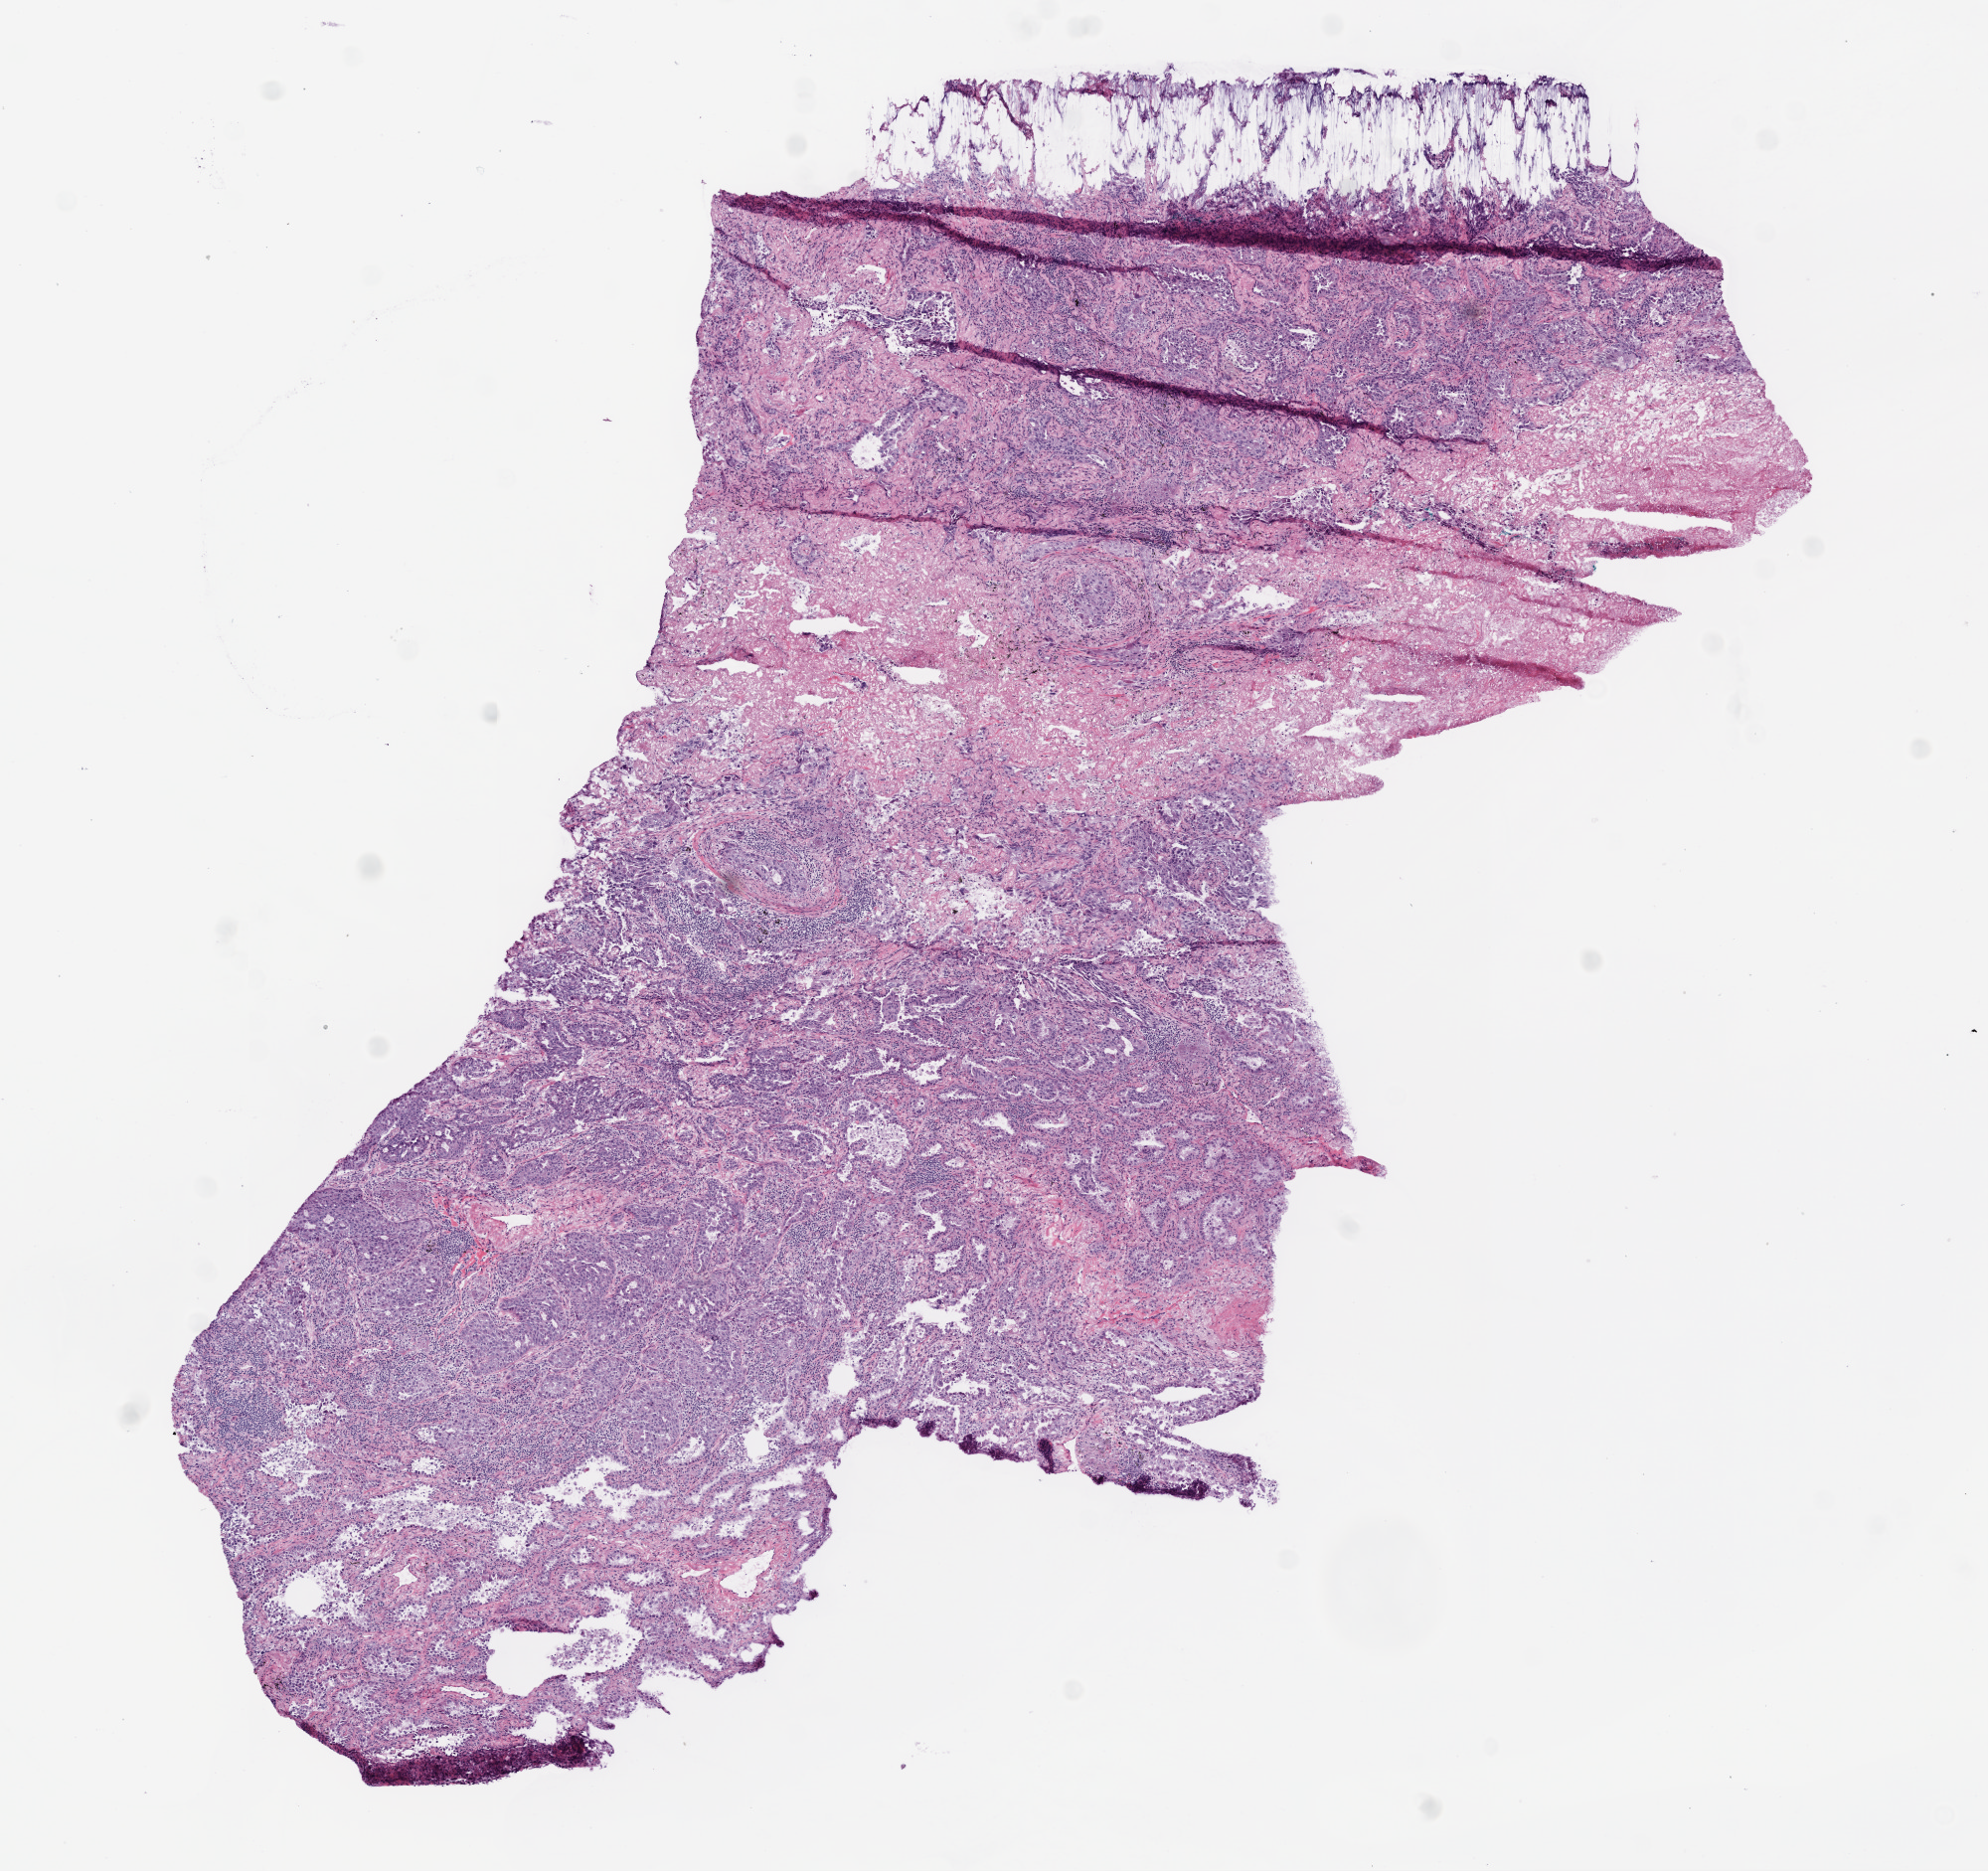
Whole-slide histology image, H&E-stained, low-resolution overview of the scanned area, about 8.0 x 7.6 mm. Frozen section. Lung, primary tumour sample. Female patient; age at initial diagnosis 71 years. Composition of this section per pathologist review: tumour cells 85%, tumour nuclei 70%.
Pathologic diagnosis: Adenocarcinoma, NOS.